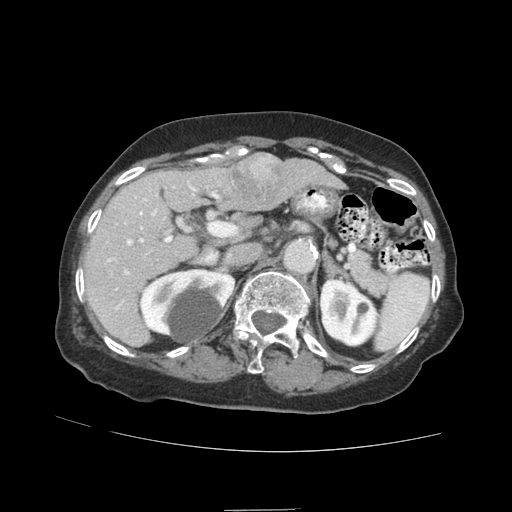
Contrast-enhanced abdominal CT (liver protocol), one axial slice; position 52 of 89 along the scan axis; soft-tissue window (W 400 / L 40 HU); 2.5 mm slice thickness; 512 × 512 image matrix, field of view 360 × 360 mm. From the clinical record (not read from this slice): diagnosis: hepatocellular carcinoma (patient treated with transarterial chemoembolisation; whether this scan precedes or follows treatment is not stated here); TNM stage (as recorded): Stage-II; Child-Pugh class: A; tumour differentiation: moderately differentiated.
Structures marked on this image (semi-automatically segmented with operator editing):
- liver parenchyma outside the tumour (the mass and vessels are separate outlines, so this box may not span the whole liver): bounding box (x1, y1, x2, y2) in pixels: (84, 158, 342, 346)
- mass: (229, 153, 292, 210)
- liver vessels: (107, 181, 197, 310)